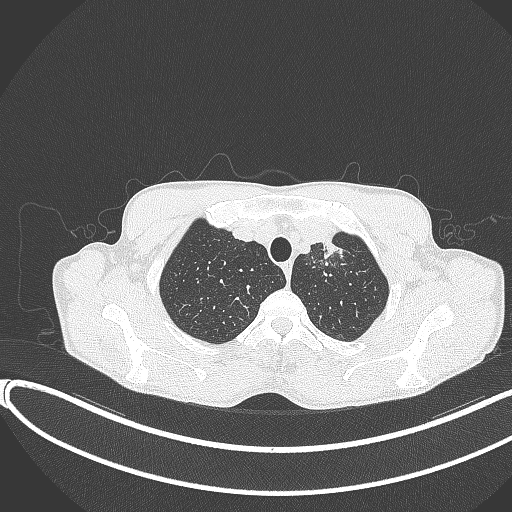
Chest CT, one axial slice; reconstruction kernel B70f; lung window (W 1500 / L -600 HU); 1 mm slice thickness; 512 × 512 image matrix, field of view 400 × 400 mm. Male patient, age 58 years. From the clinical record (not read from this slice): clinical TNM (as recorded): T1c N1 M0.
Outlined on this slice (rectangle marked by the reading radiologist):
- lung tumour (recorded histology: adenocarcinoma): bounding box <314,227,349,266> (left, top, right, bottom; pixels)